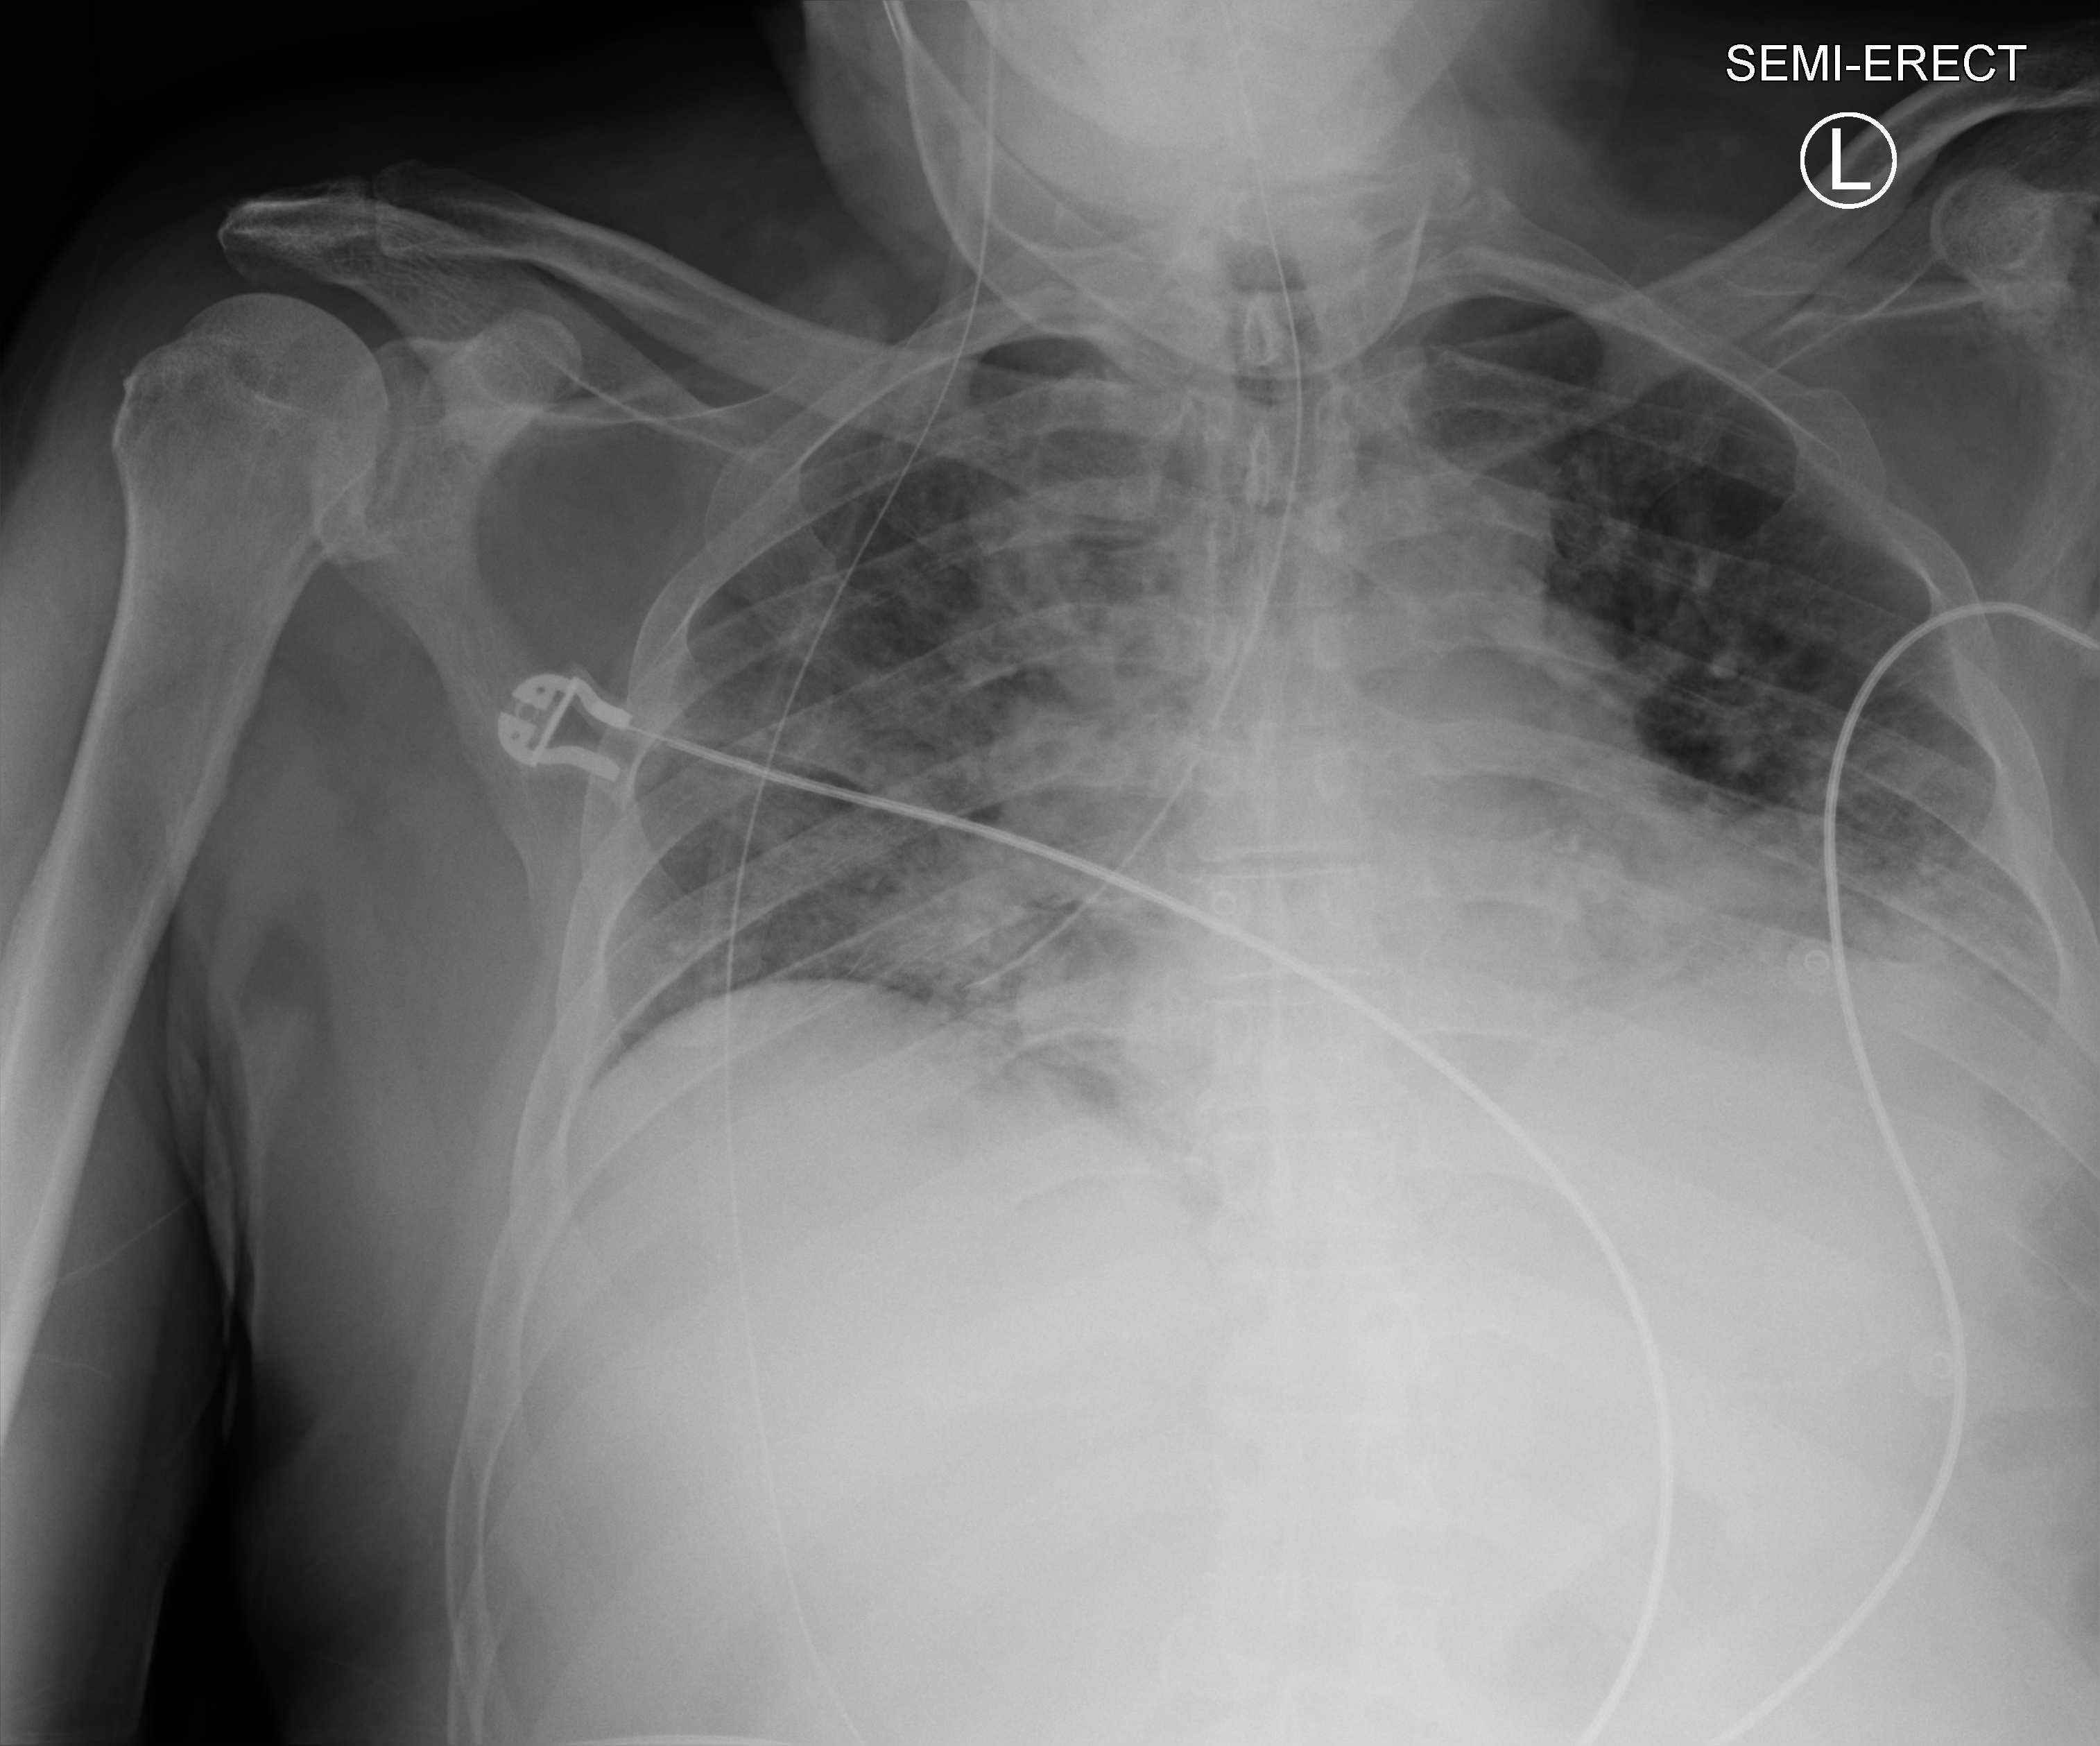
Portable chest radiograph; anteroposterior (AP) projection. Male patient hospitalised with COVID-19, age 60–74 years.
Admission-level facts for this patient (not findings on this image; timing relative to this image not recorded): other chronic lung disease (admission record): no.